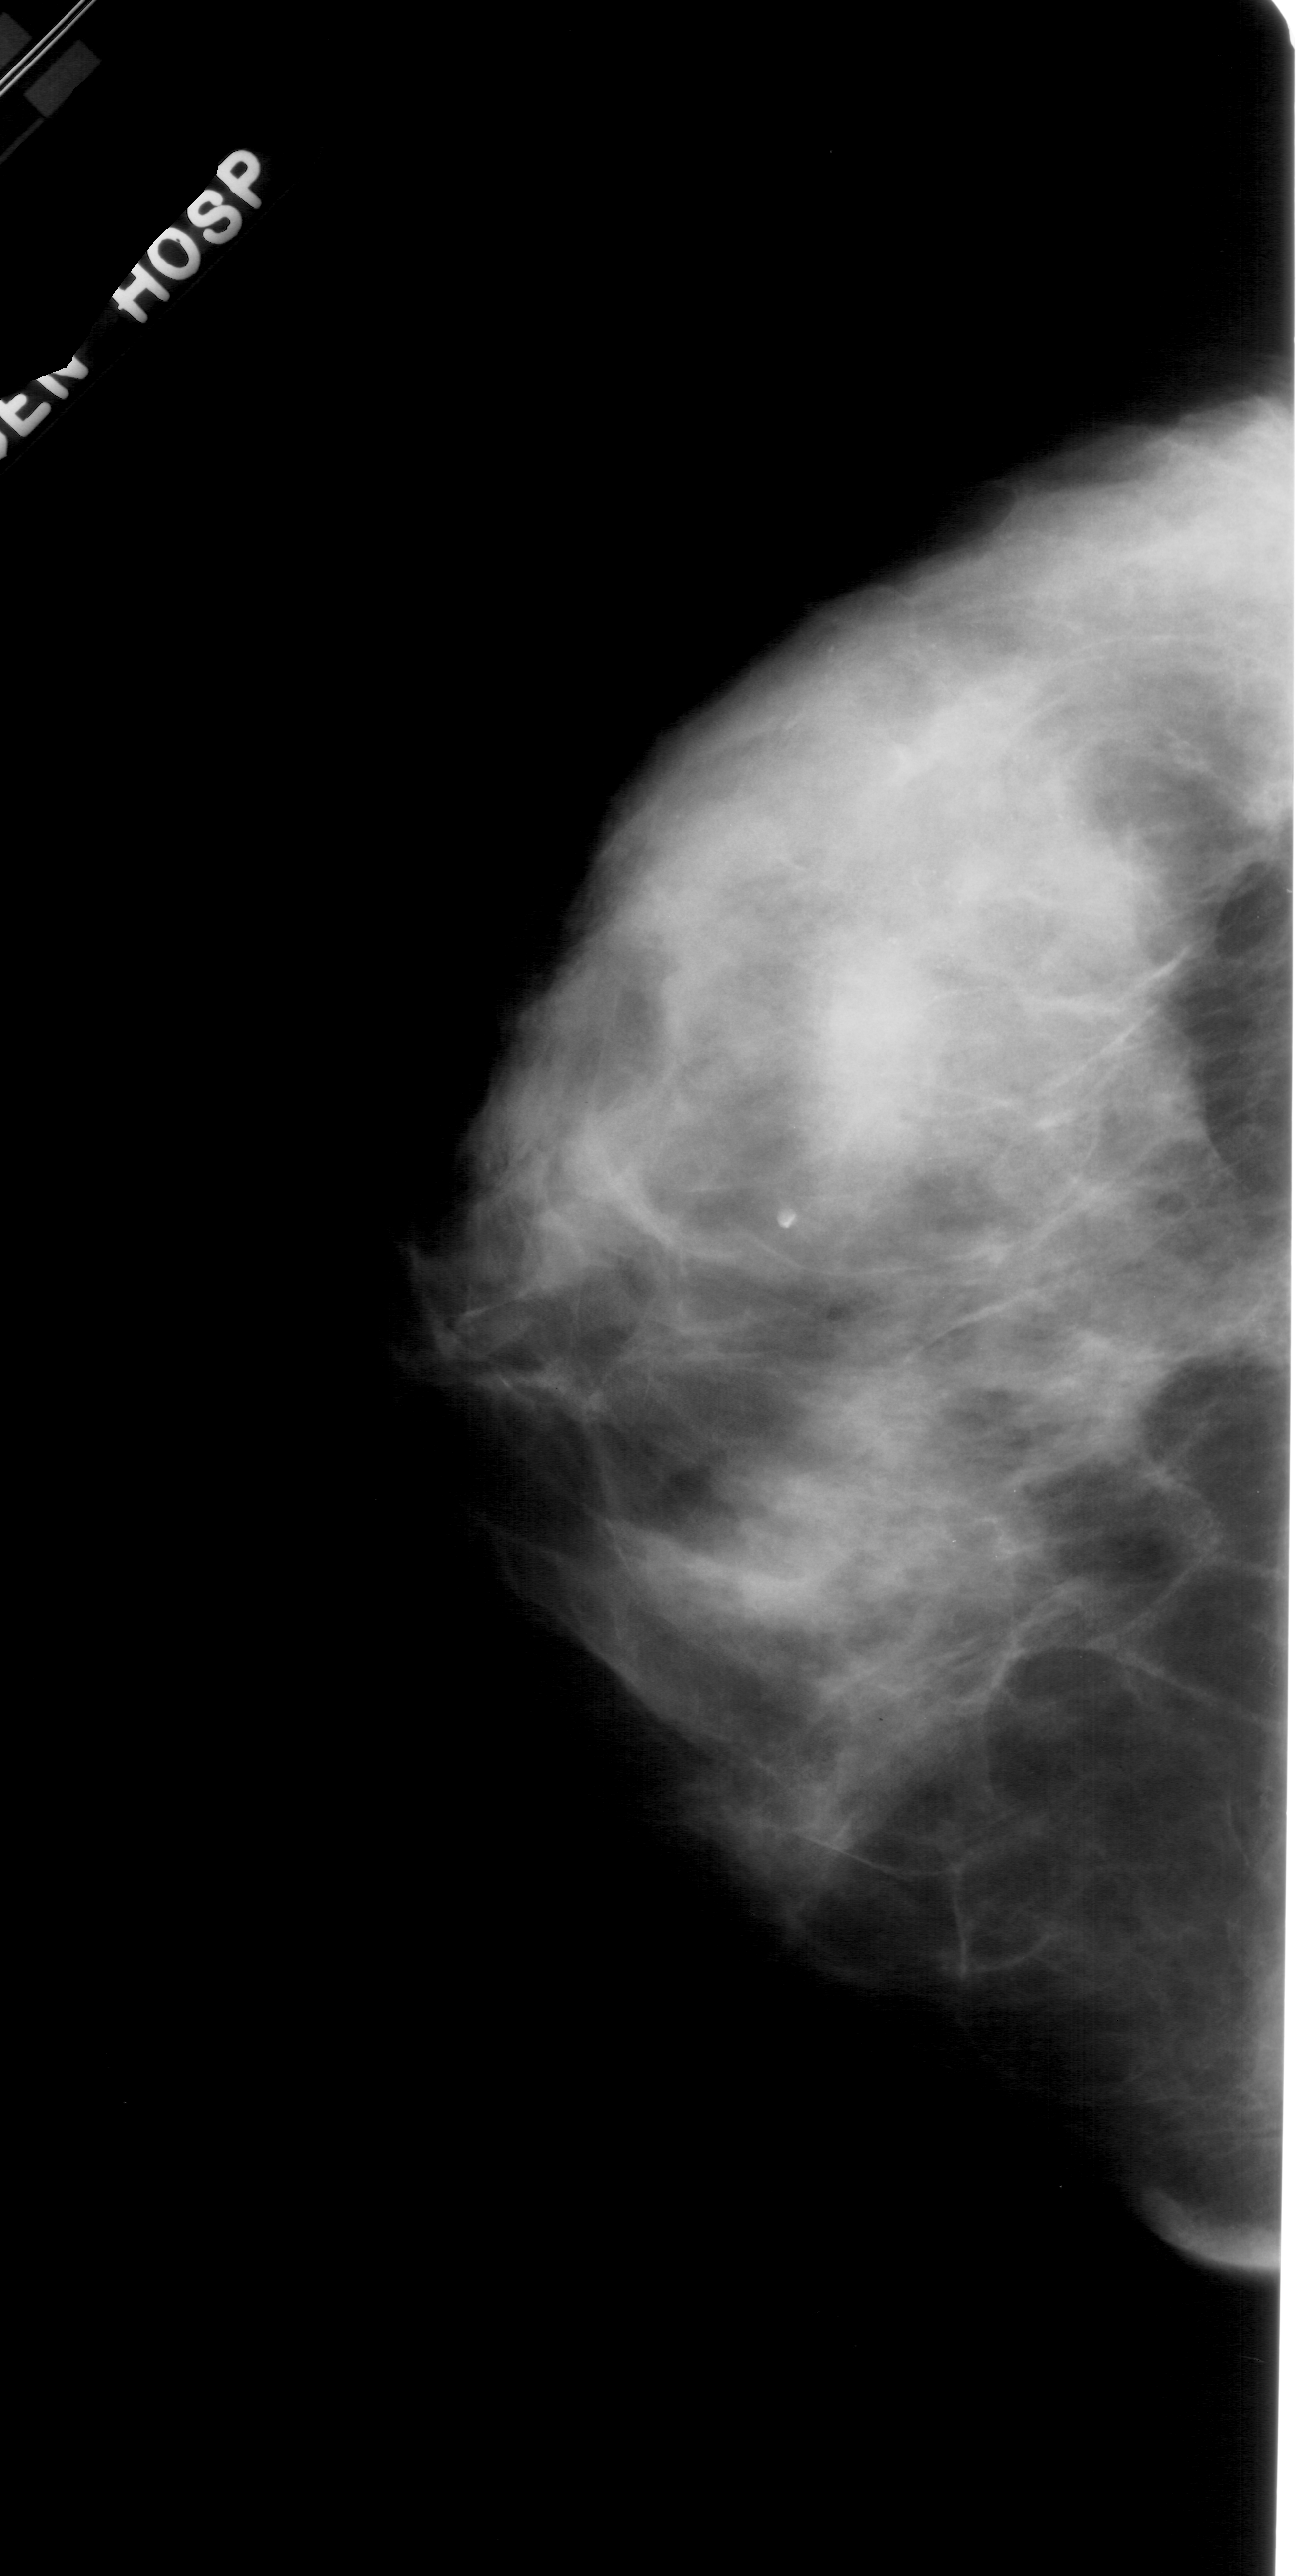
Mammogram (digitized film); left breast; craniocaudal (CC) view; BI-RADS breast density category 4 (scale 1–4).
Abnormality record for this image: calcifications, morphology punctate, distribution segmental; BI-RADS assessment category 4; subtlety rating 2 on a 1 (subtle) to 5 (obvious) scale; pathology result (as recorded, not read from the image): benign.